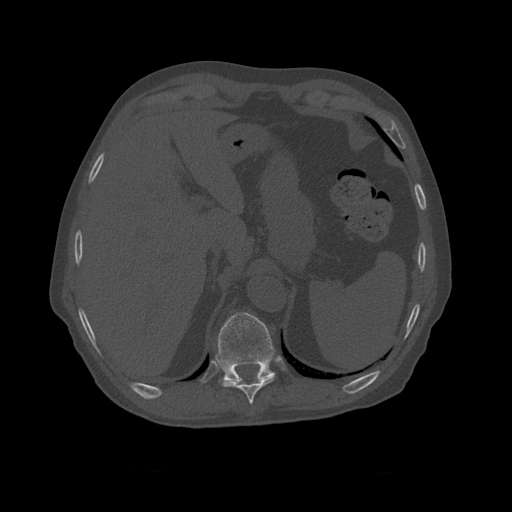
CT including the spine, one axial slice. Slice 412 of 450 in the series (ordered by position). Reconstruction kernel STANDARD. Bone window (W 1800 / L 400 HU). 1.25 mm slice thickness. 512 × 512 image matrix, field of view 405 × 405 mm. Patient age 75 years. From the clinical record (not read from this slice): primary cancer: prostate.
Outlined on this slice (semi-automatic segmentation, software-assisted and operator-edited):
- T10 vertebra: bounding box <215,312,275,383> (left, top, right, bottom; pixels)
- T9 vertebra: <221,379,274,405>